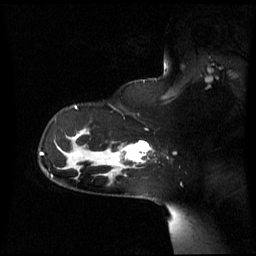
Breast MRI (dynamic contrast-enhanced), one sagittal slice; slice 45 of 60 in the series (ordered by position); dynamic contrast-enhanced series, image 2 of 3 at this slice position (ordered by acquisition); 1.5 T; TE 4.2 ms, TR 8.4 ms; 256 × 256 image matrix, field of view 270 × 270 mm. Female patient, age 39 years. From the clinical record (not read from this slice): setting: breast cancer imaged before/during neoadjuvant chemotherapy; receptor status: triple-negative.
Annotated regions visible in this slice (semi-automatically segmented with operator editing):
- analysis volume of interest (the breast-tissue region the enhancement analysis was run in; not a lesion): bounding box <101,141,150,173> (left, top, right, bottom; pixels)
- tumour enhancement mask (voxels above the 70 % enhancement threshold inside the analysis volume of interest): <112,141,149,164>